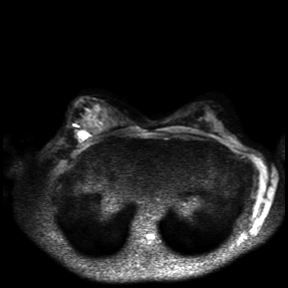
Breast MRI, one axial slice; position 20 of 30 along the scan axis; diffusion-weighted series; image 2 of 4 stored at this slice position (different b-values; order by instance number); 3 T; 4 mm slice thickness; 288 × 288 image matrix, field of view 360 × 360 mm. Female patient.
Structures marked on this image (manually delineated by an expert):
- tumour on diffusion-weighted imaging: box from (x=78, y=130) to (x=87, y=139) px